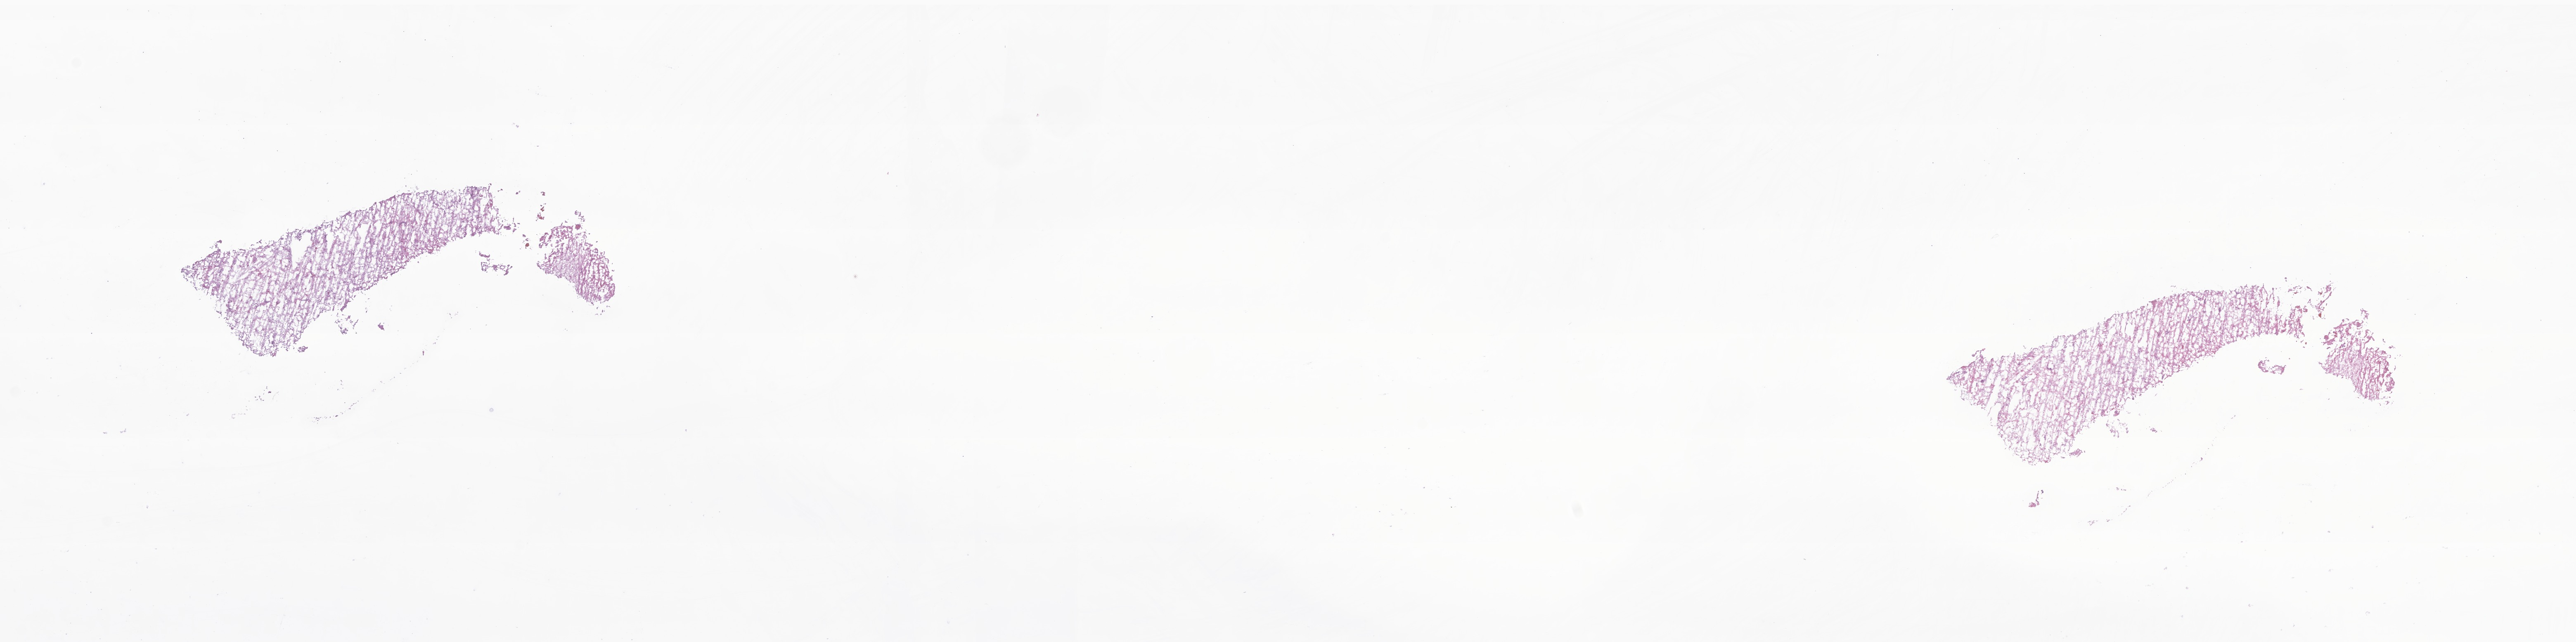
Digitized hematoxylin and eosin (H&E)-stained section of tumor tissue from the brain, low-resolution overview of the scanned area, about 26.3 x 6.6 mm, frozen section (OCT-embedded). Female patient, age 133 months (11 years 1 month).
Recorded diagnosis: Tumor cells, uncertain whether benign or malignant.